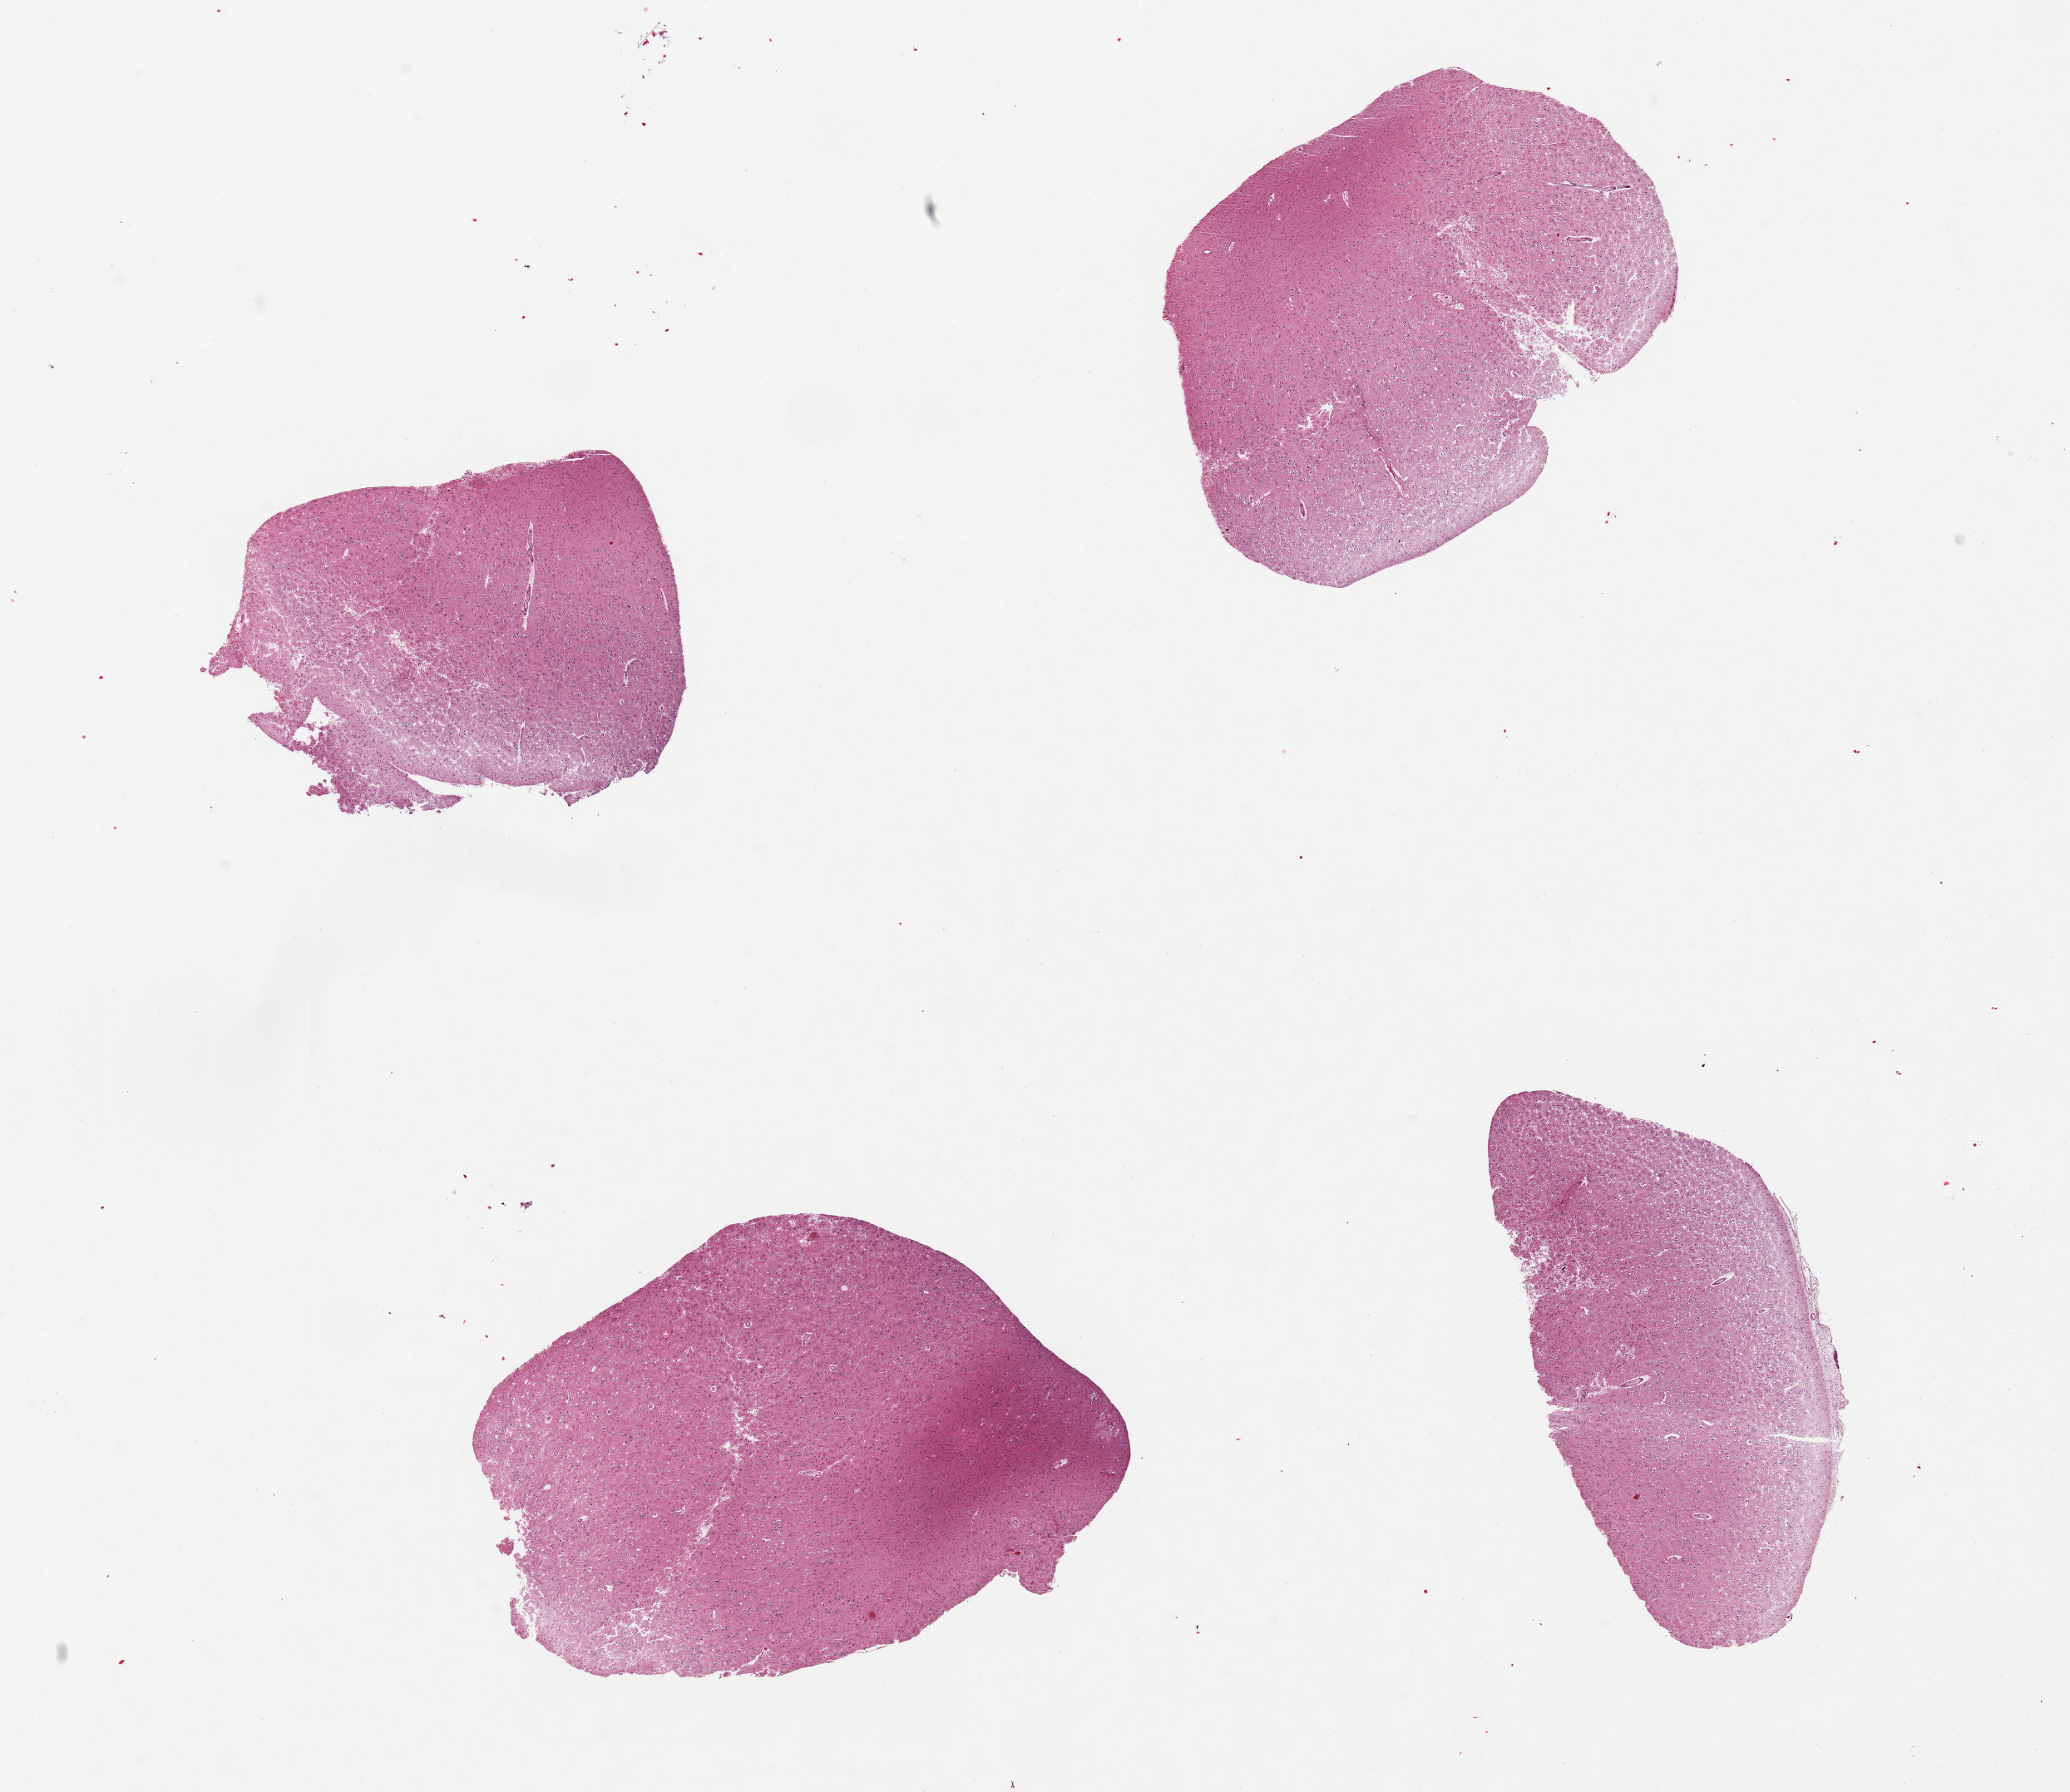
Whole-slide image, haematoxylin and eosin stain, brightfield, a low-resolution overview of the entire scanned area, about 19.7 x 17.0 mm; PAXgene-fixed paraffin-embedded (PFPE) section; target tissue: cerebral cortex; donor tissue sample. Donor sex: male.
Review note (as recorded): 4 pieces, mild autolysis.